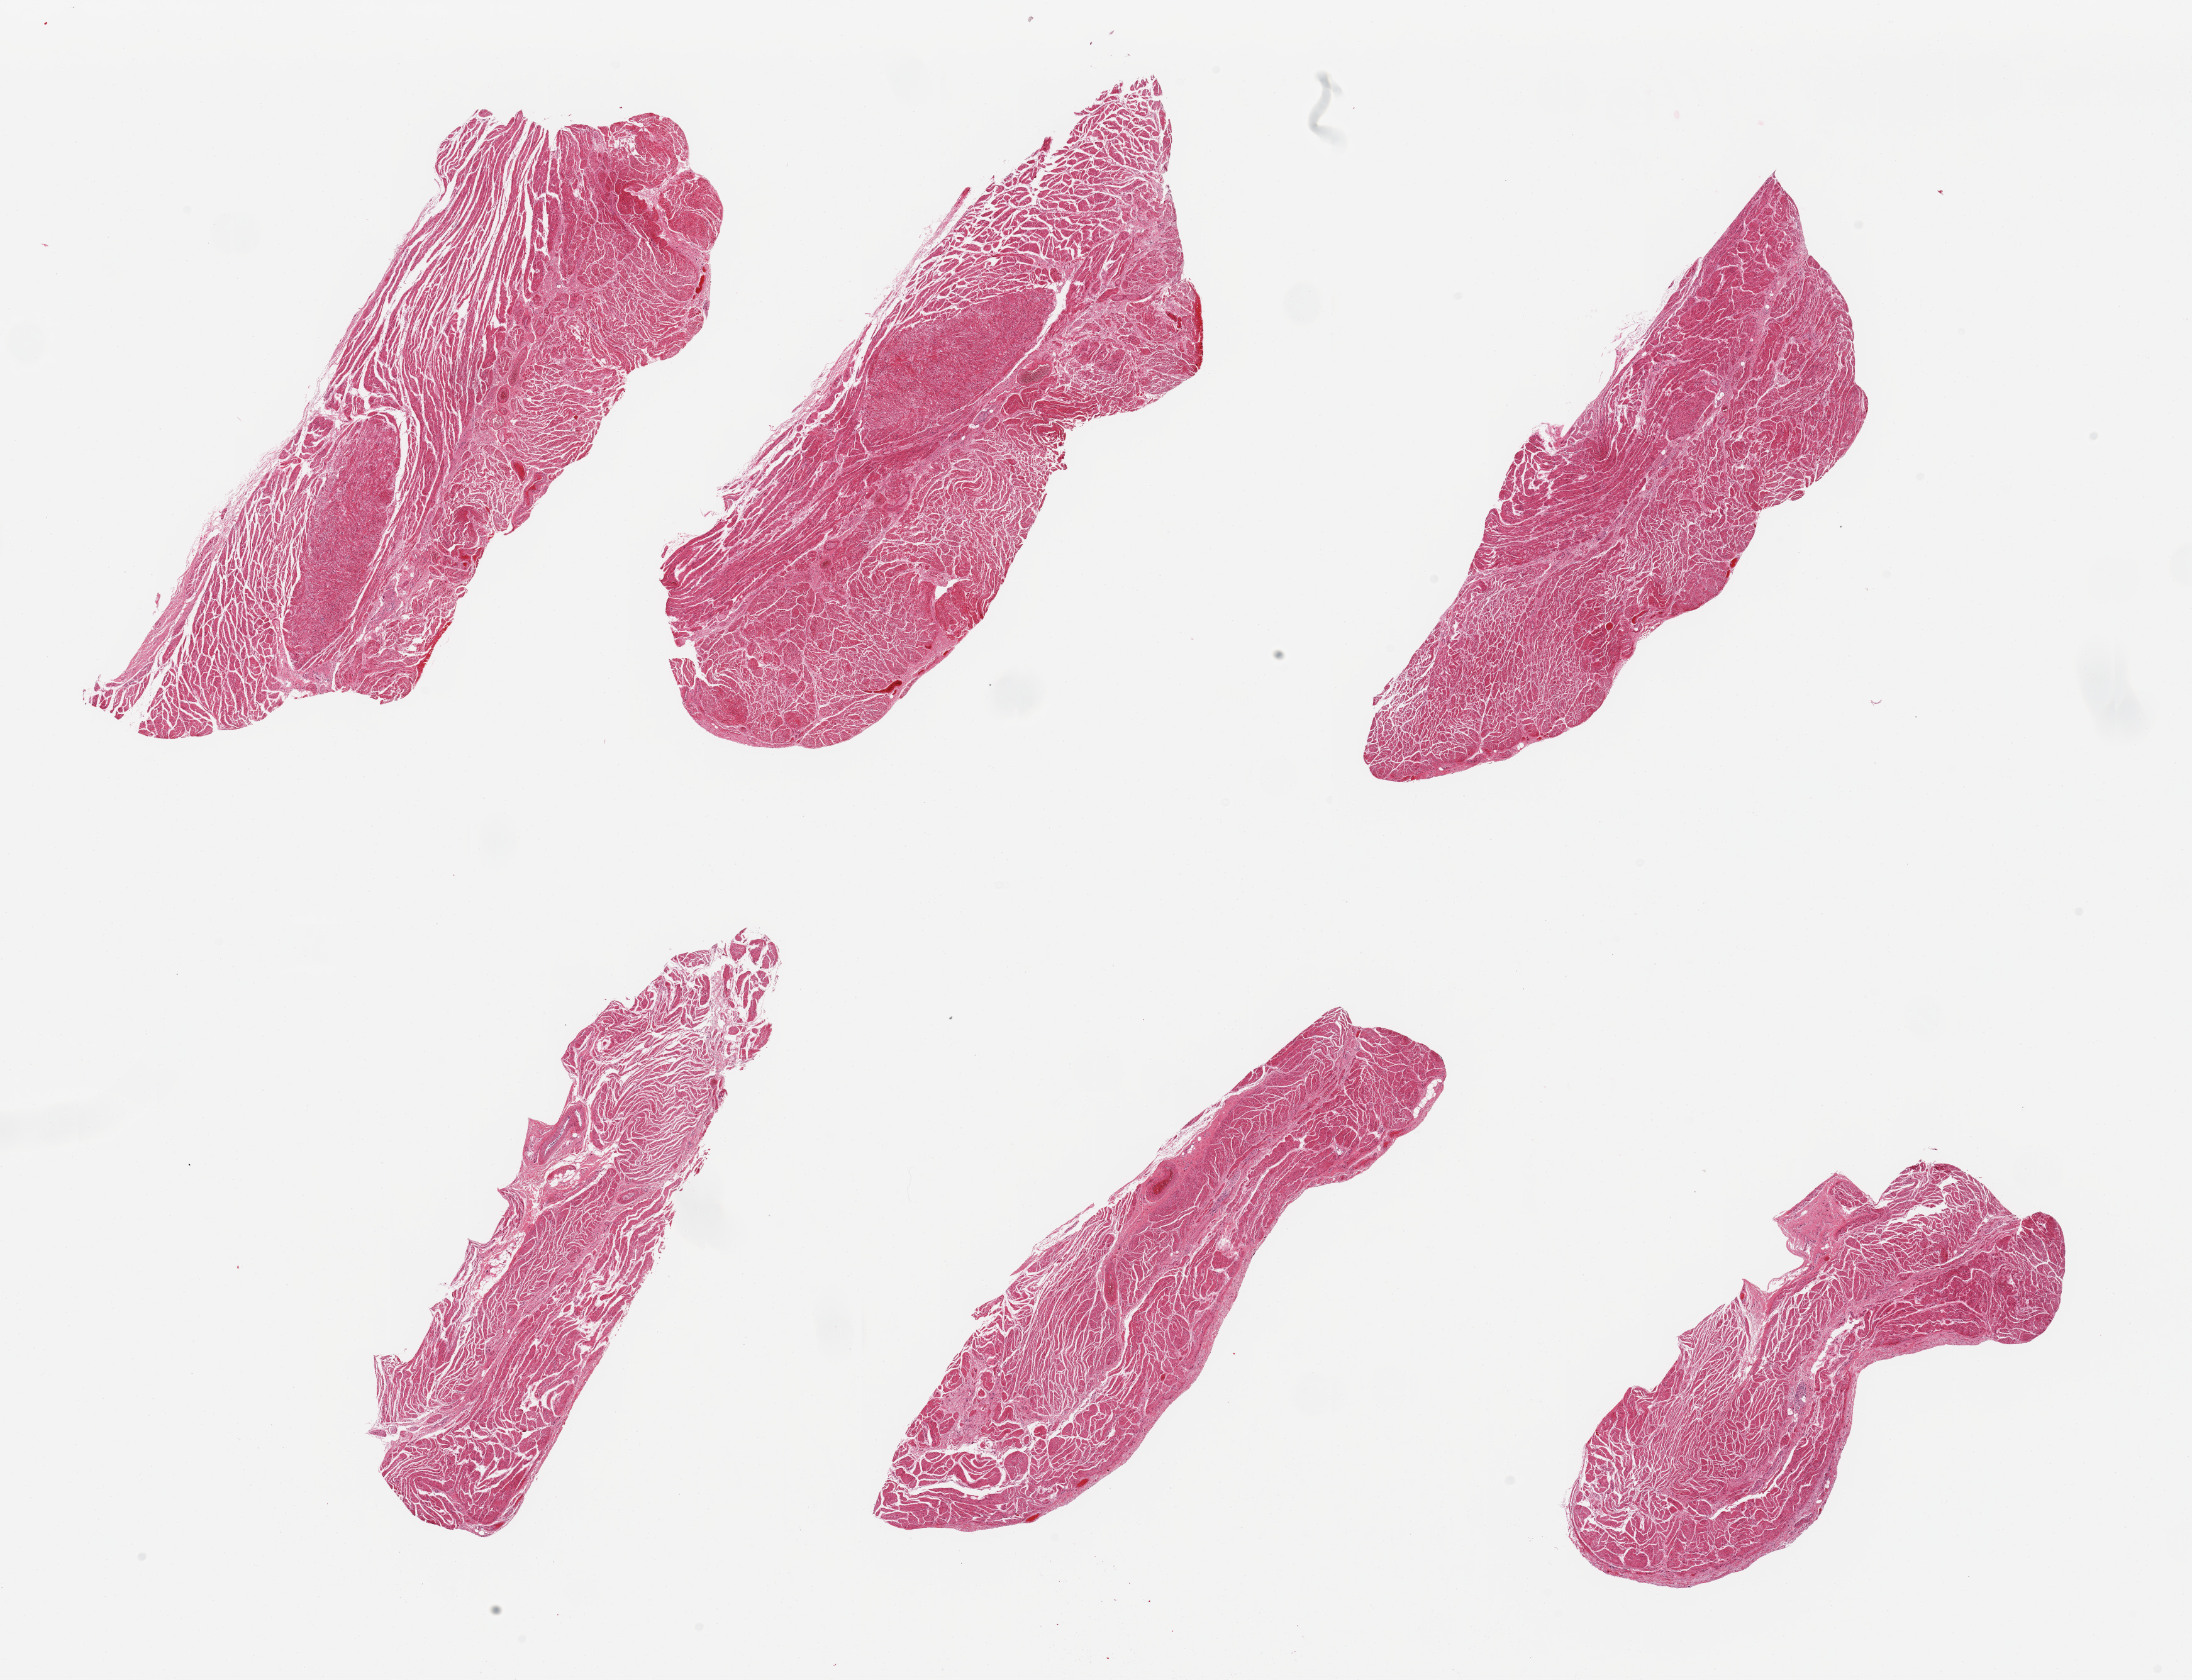
Whole-slide image, hematoxylin and eosin (H&E) stain — low-resolution overview of the scanned area, about 27.6 x 21.1 mm. PAXgene-fixed paraffin-embedded (PFPE) section. Target tissue: gastroesophageal junction. Tissue donor sample.
- review note (as recorded): 6 pieces; well trimmed, small leiomyoma